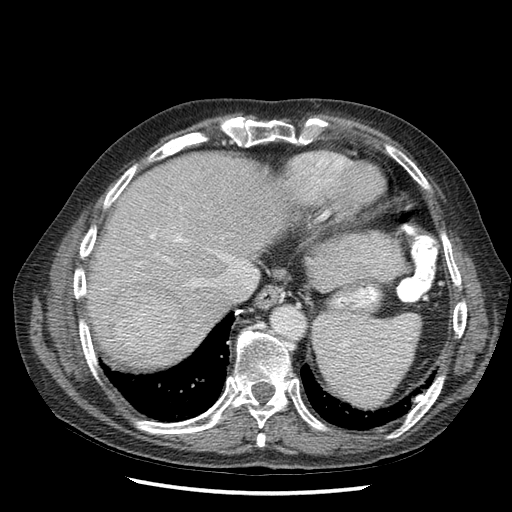
Contrast-enhanced abdominal CT (liver protocol), one axial slice; position 54 of 67 along the scan axis; reconstruction kernel STANDARD; 120 kVp; soft-tissue window (W 400 / L 40 HU); 2.5 mm slice thickness; 512 × 512 image matrix, field of view 360 × 360 mm. Case-level facts recorded for this patient, not image findings: diagnosis: hepatocellular carcinoma (patient treated with transarterial chemoembolisation; whether this scan precedes or follows treatment is not stated here); TNM stage (as recorded): Stage-I.
Structures marked on this image (semi-automatic segmentation, software-assisted and operator-edited):
- abdominal aorta: bounding box (x1, y1, x2, y2) in pixels: (273, 306, 304, 336)
- liver parenchyma outside the tumour (the mass and vessels are separate outlines, so this box may not span the whole liver): (88, 152, 288, 361)
- mass: (110, 285, 181, 360)
- liver vessels: (135, 233, 156, 270)